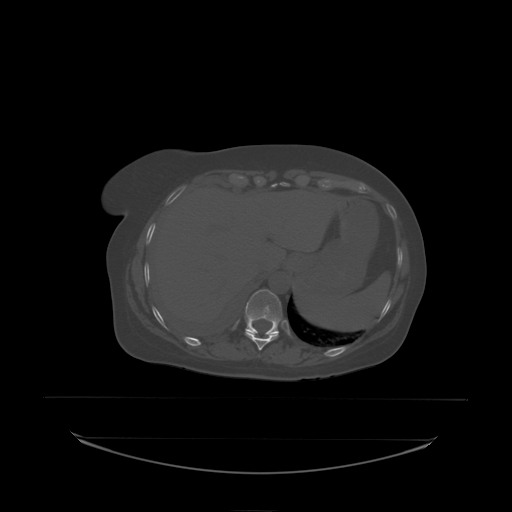
CT including the spine, one axial slice. Position 109 of 242 along the scan axis. Bone window (W 1800 / L 400 HU). 2.5 mm slice thickness. 512 × 512 image matrix, field of view 500 × 500 mm. Patient: female, 53 years. From the clinical record (not read from this slice): primary cancer: lung; vertebrae with lytic lesions (as recorded): T7, L1.
Outlined on this slice (semi-automatically segmented with operator editing):
- T10 vertebra: bounding box <245,333,278,338> (left, top, right, bottom; pixels)
- T11 vertebra: <246,290,283,335>